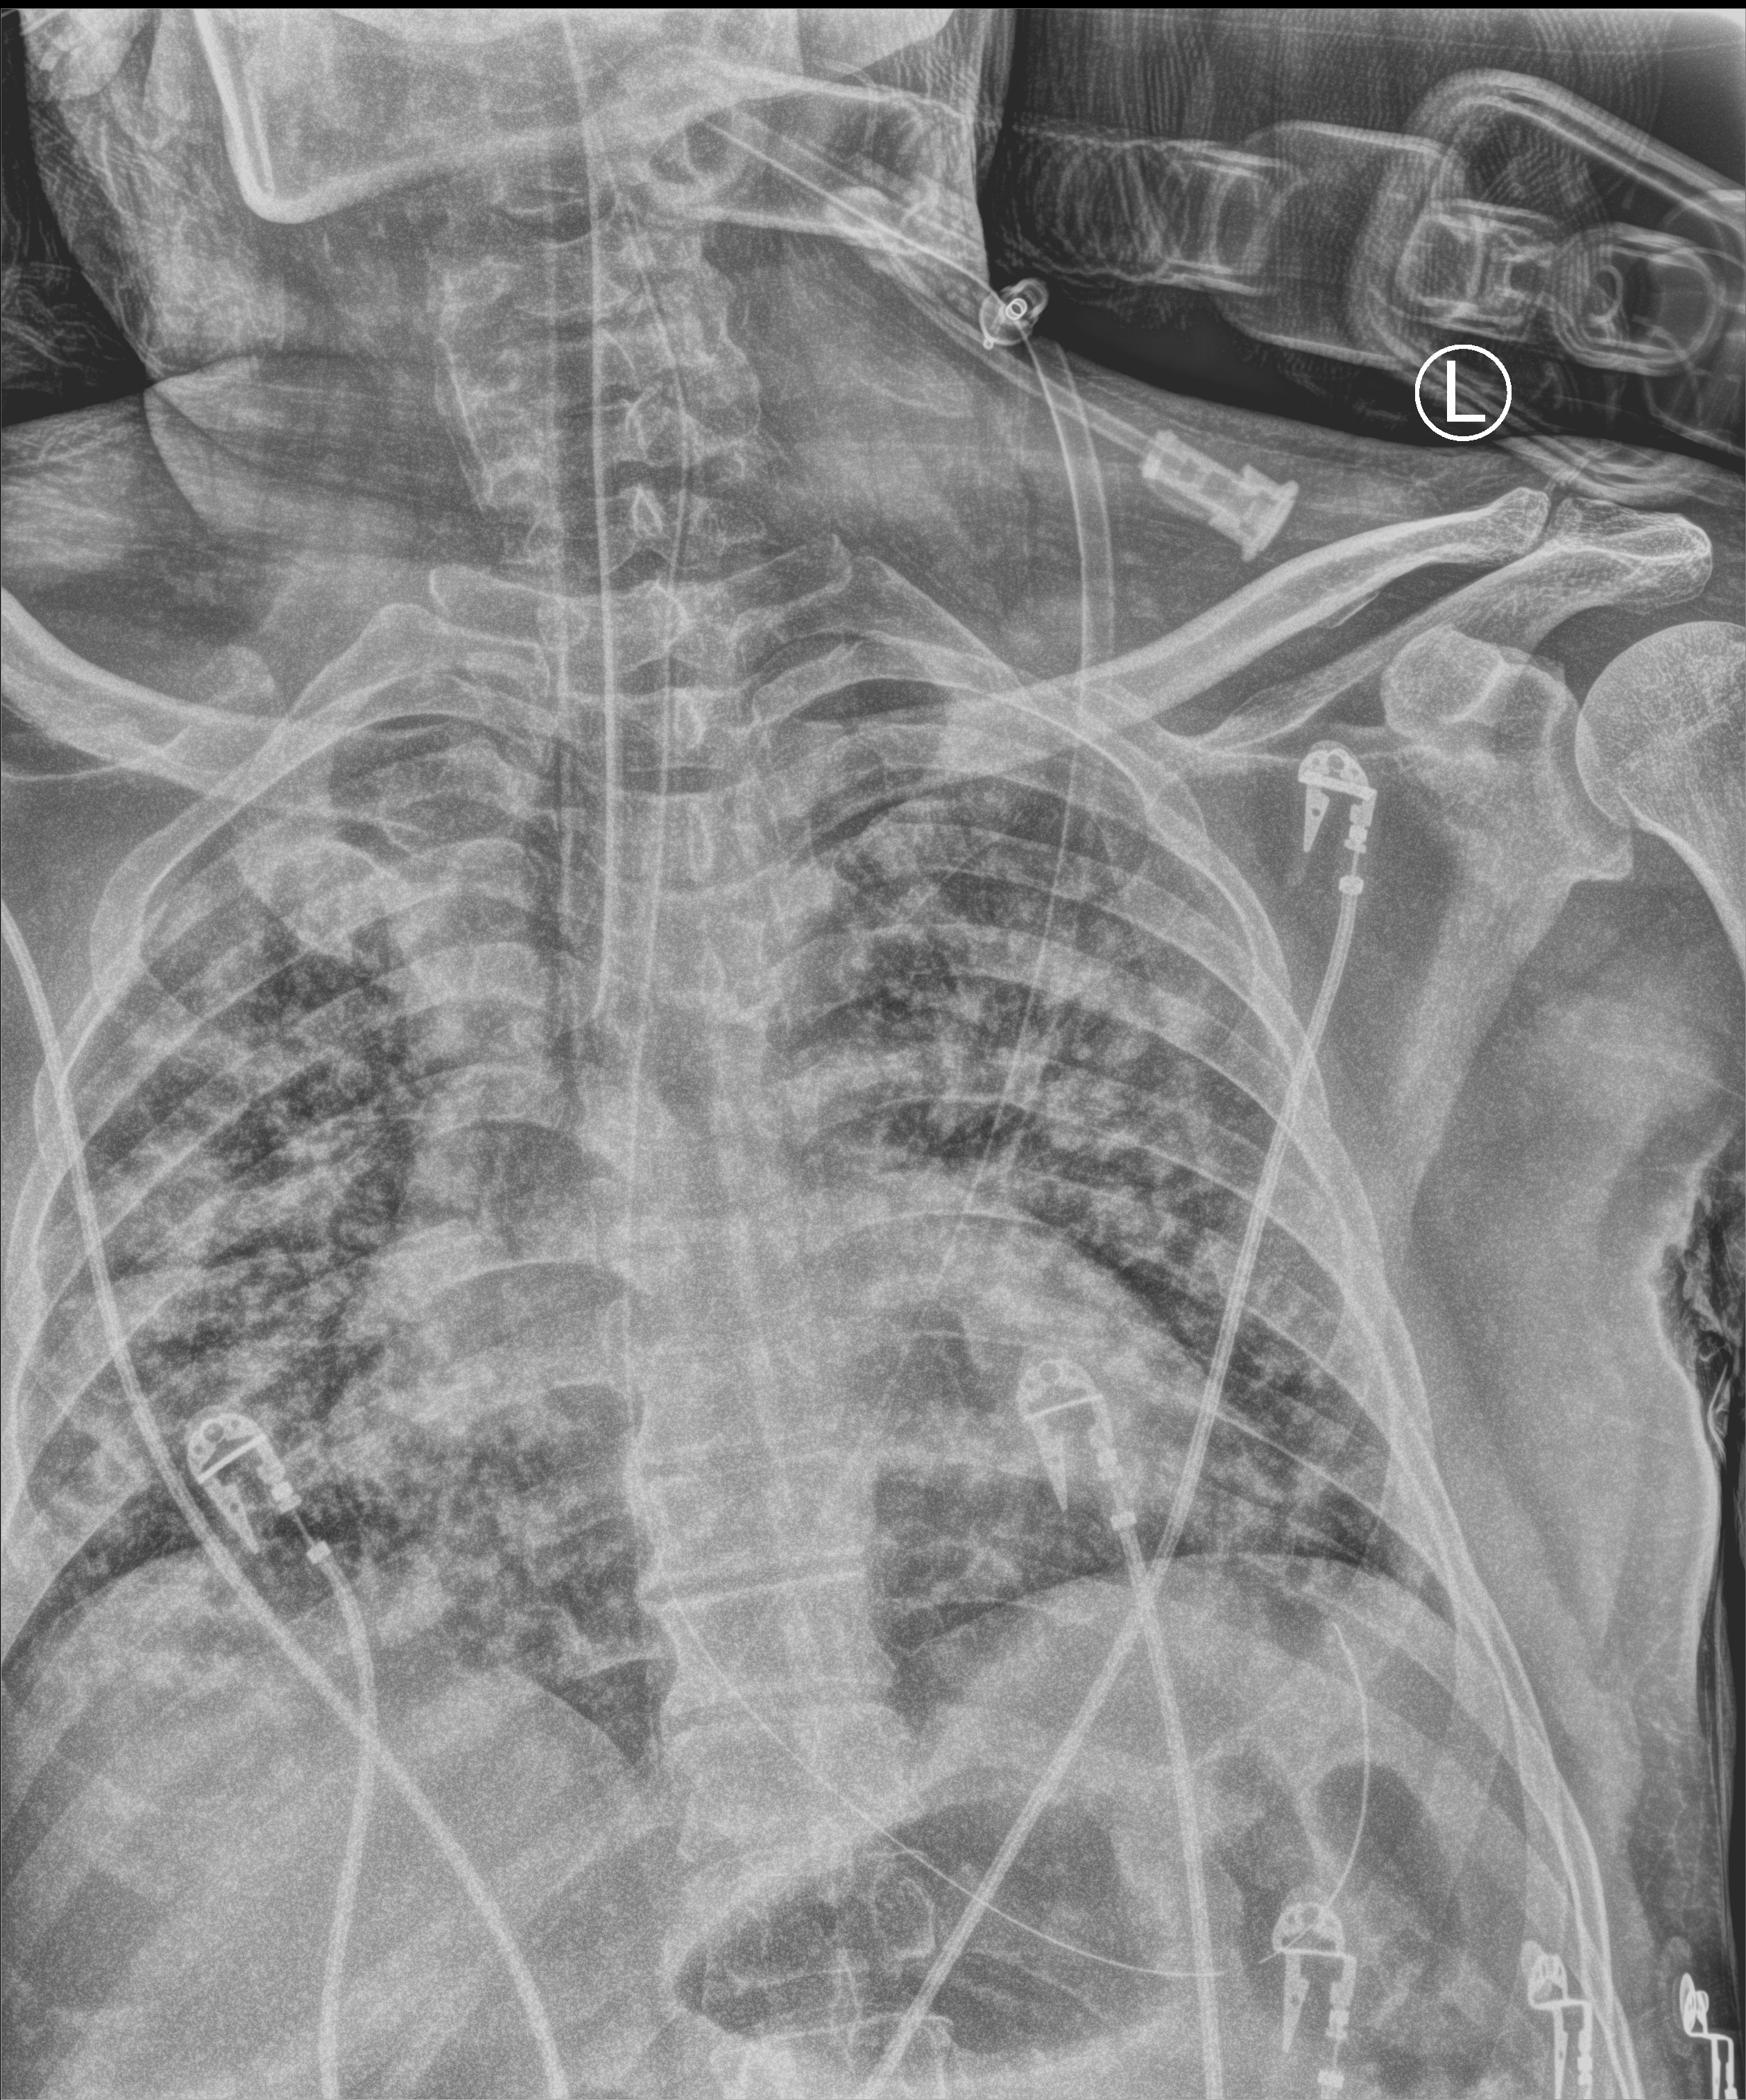
Bedside chest radiograph (computed radiography); anteroposterior (AP) projection. Patient hospitalised with COVID-19; male, aged 18–59 years.
Admission-level facts for this patient (not findings on this image; timing relative to this image not recorded): hypertension (admission record): yes; mechanically ventilated during this hospital stay: yes; admitted to intensive care during this hospital stay: yes.